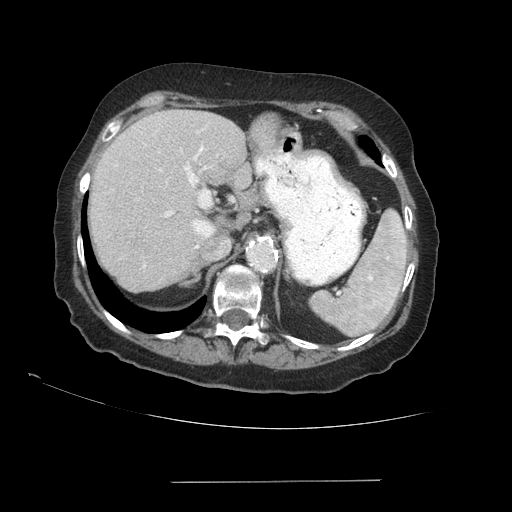
Contrast-enhanced abdominal CT (liver protocol), one axial slice; position 64 of 89 along the scan axis; reconstruction kernel STANDARD; 140 kVp; soft-tissue window (W 400 / L 40 HU); 2.5 mm slice thickness; 512 × 512 image matrix, field of view 400 × 400 mm. Case-level facts recorded for this patient, not image findings: diagnosis: hepatocellular carcinoma (patient treated with transarterial chemoembolisation; whether this scan precedes or follows treatment is not stated here); TNM stage (as recorded): Stage-IVA; Child-Pugh class: A; tumour nodularity: uninodular.
Outlined on this slice (semi-automatically segmented with operator editing):
- liver parenchyma outside the tumour (the mass and vessels are separate outlines, so this box may not span the whole liver): bounding box (x1, y1, x2, y2) in pixels: (88, 110, 251, 290)
- liver vessels: (143, 146, 214, 267)